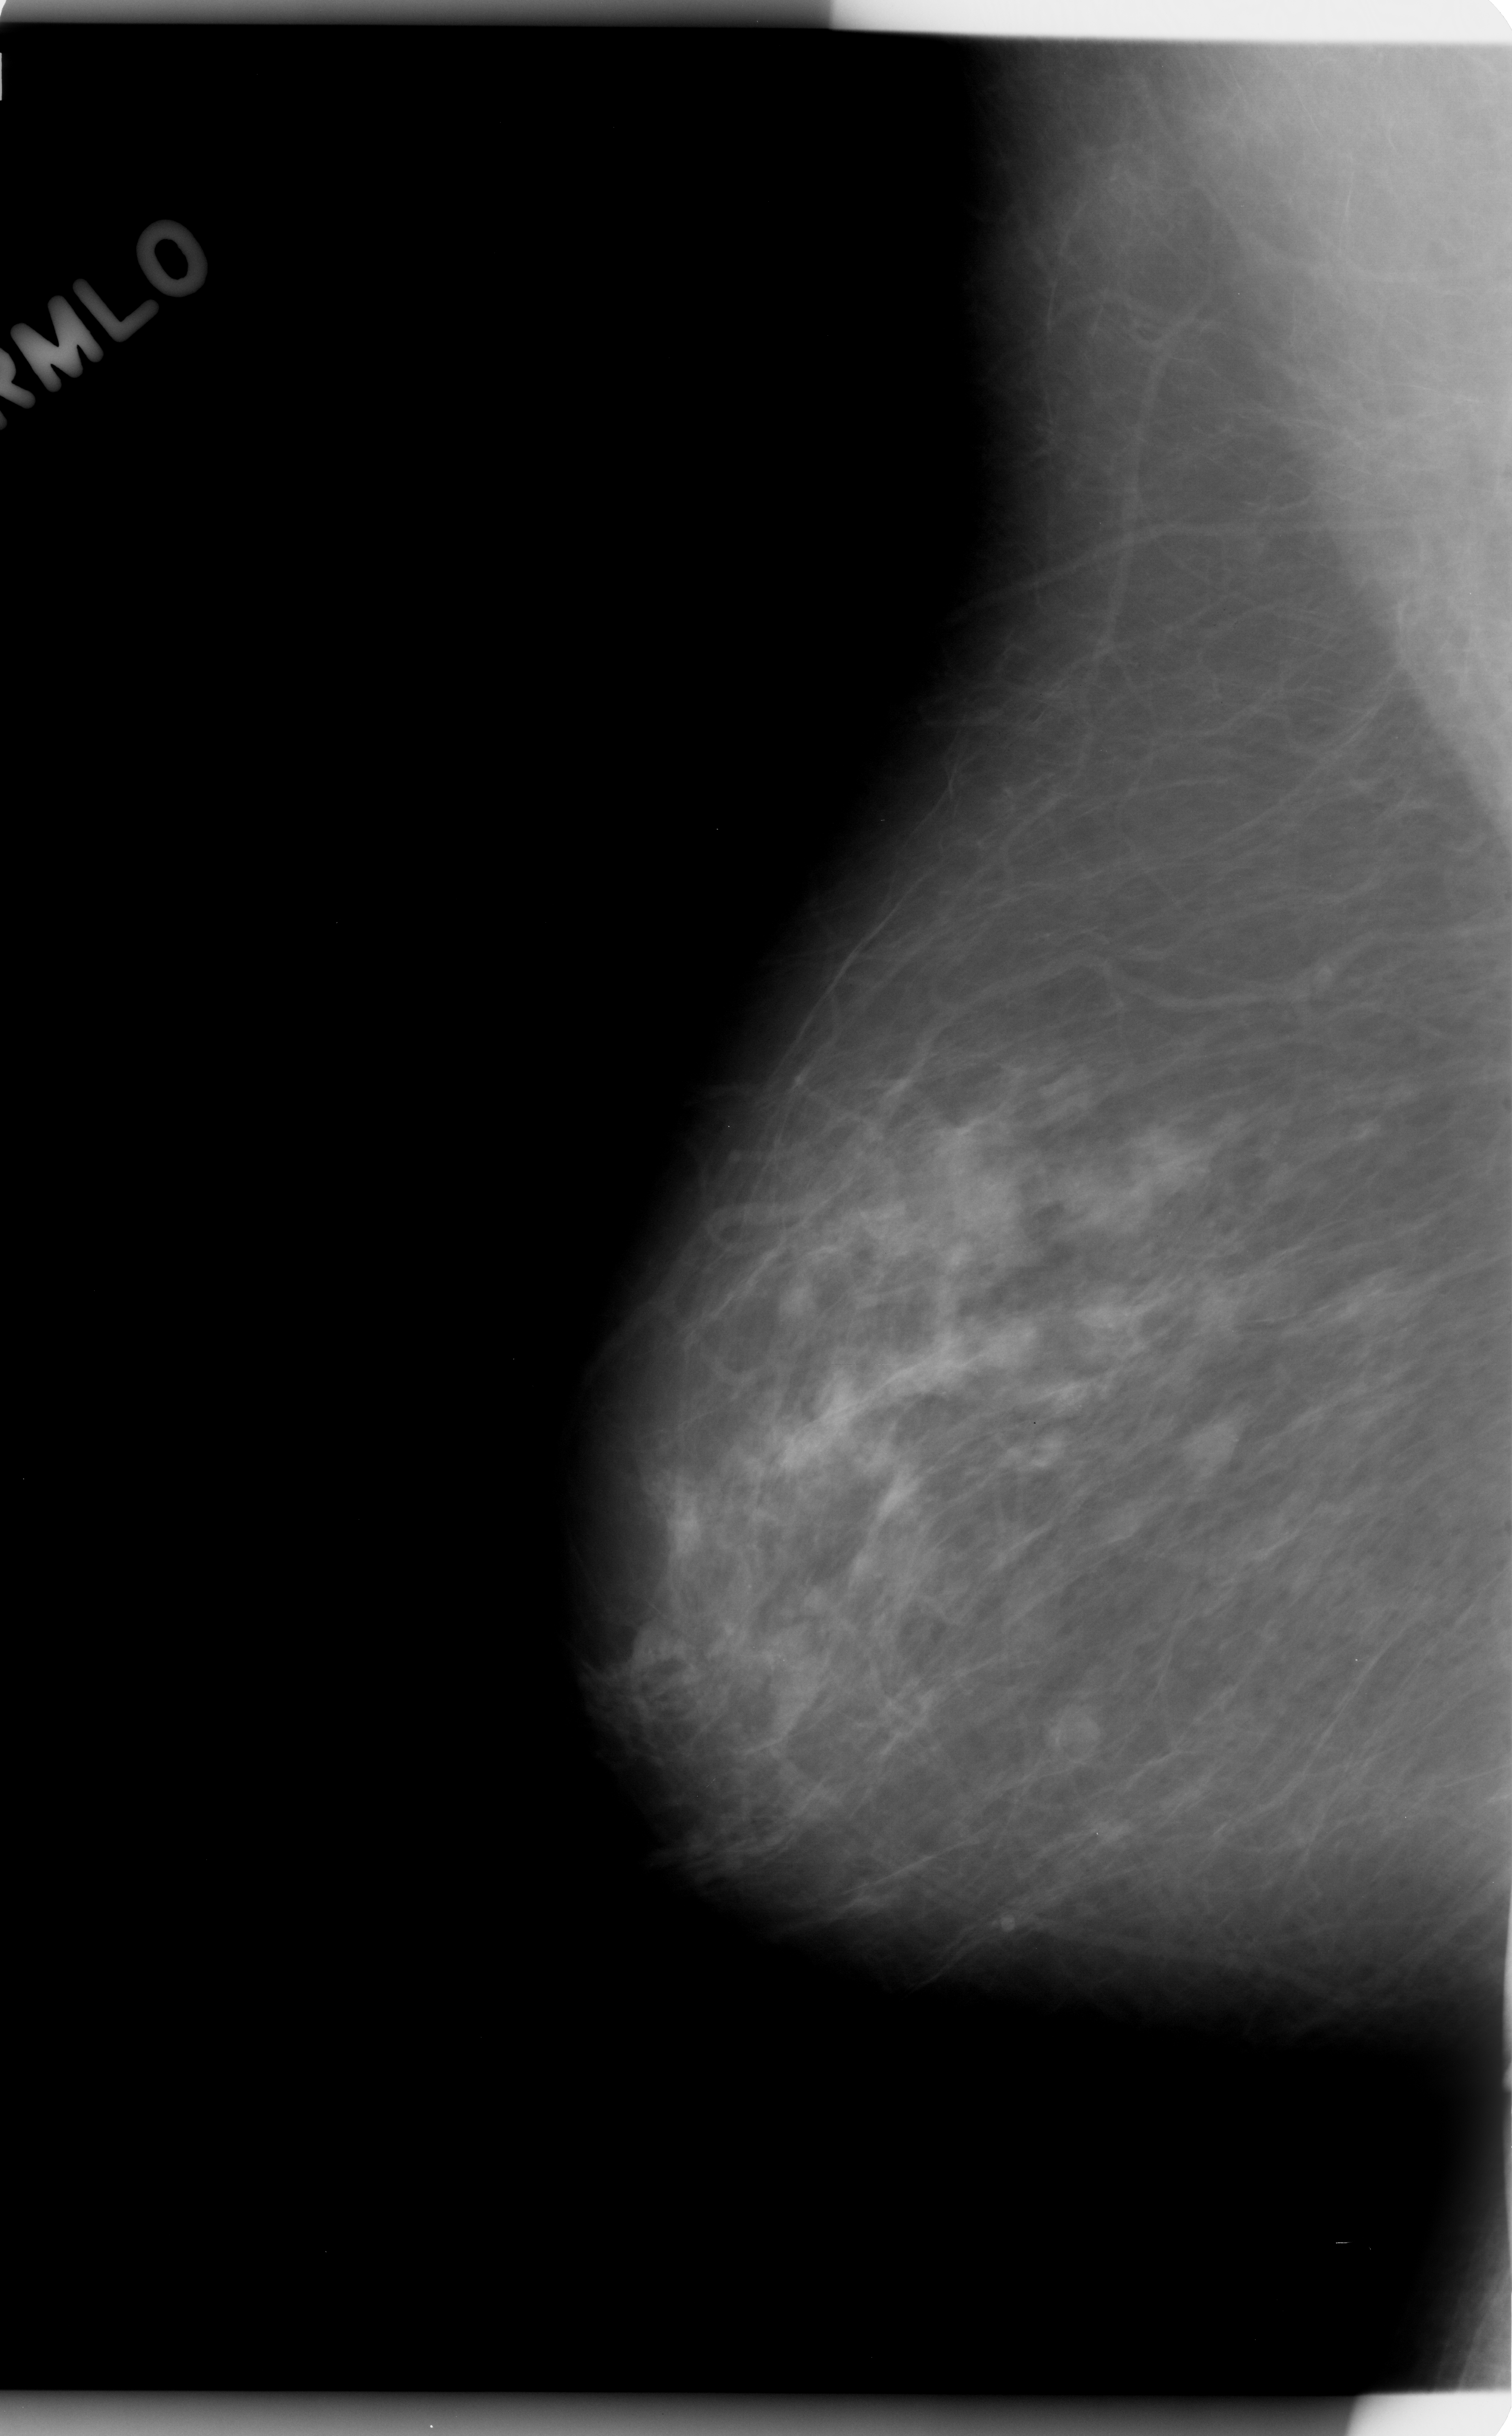
Digitized screen-film mammogram; right breast; mediolateral oblique (MLO) view; BI-RADS breast density category 1 (scale 1–4).
- Marked abnormality: calcifications, morphology amorphous, distribution regional; BI-RADS assessment category 4; subtlety rating 2 on a 1 (subtle) to 5 (obvious) scale; pathology (as recorded): benign.